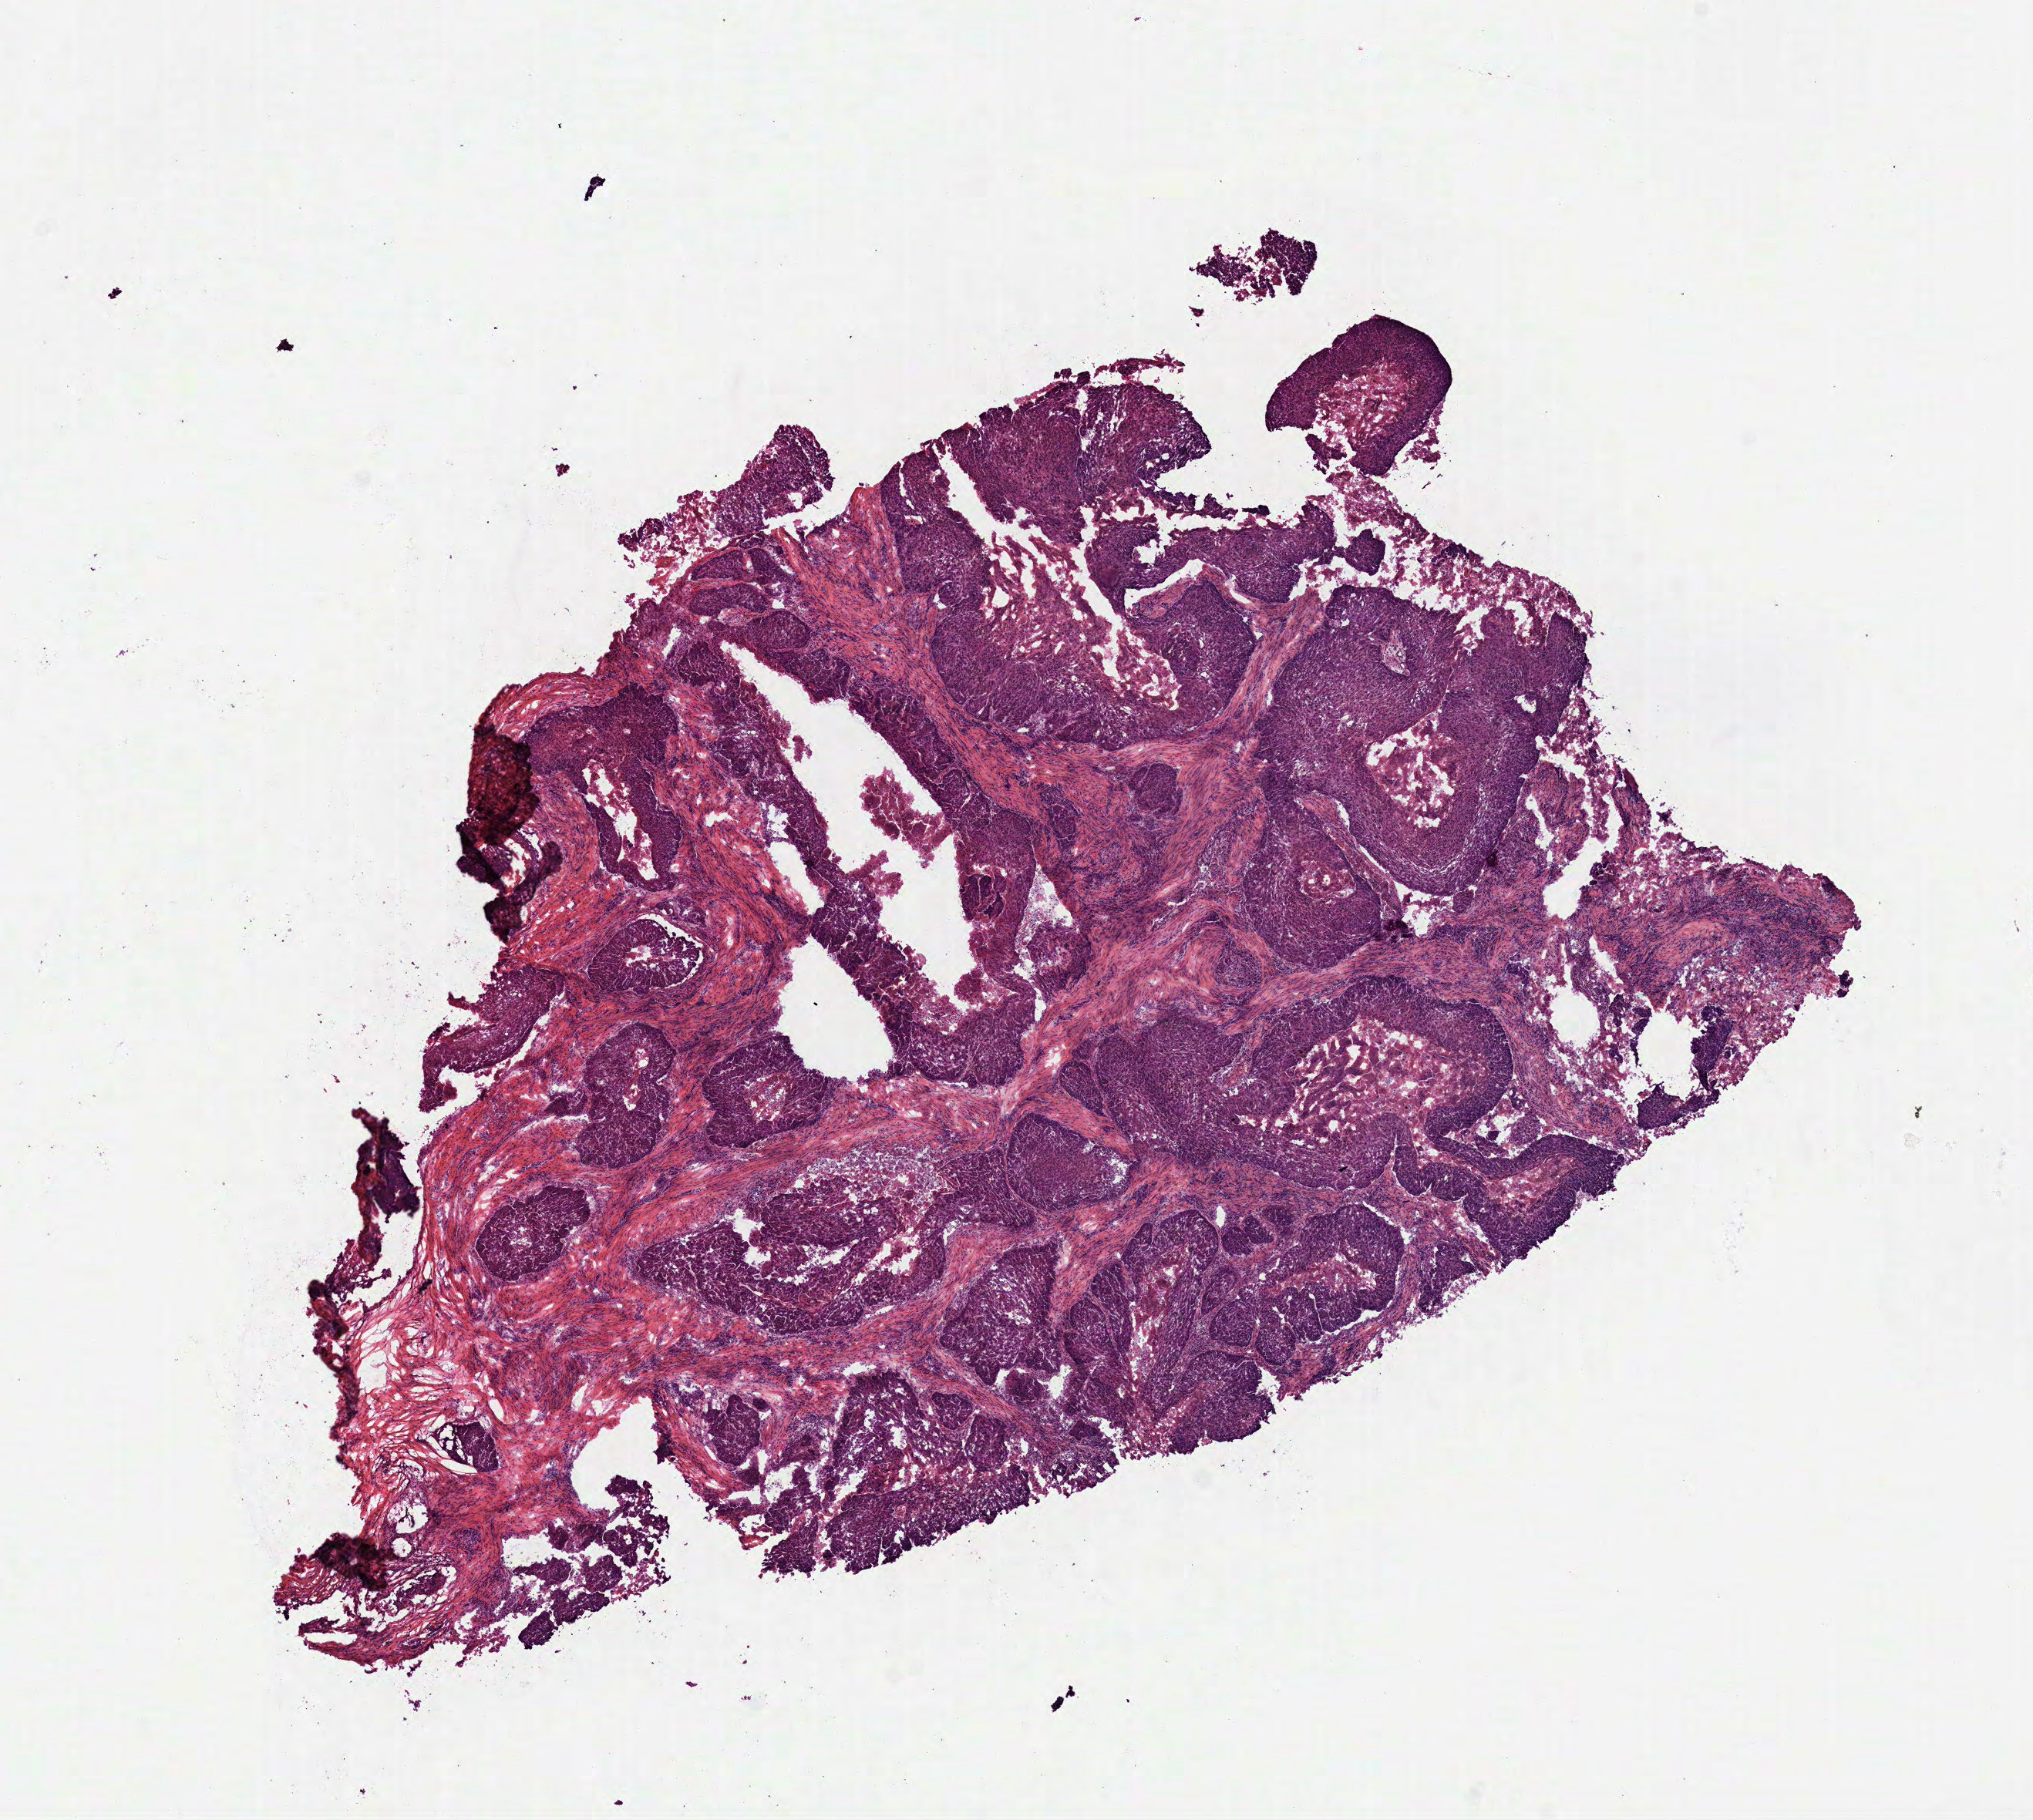
H&E whole-slide image — a low-resolution overview of the entire scanned area, about 10.6 x 9.5 mm (from a 40x scan), frozen section, primary tumour sample from the head and neck. Patient: male, age at initial diagnosis 68 years. Histologic grade: G2 (moderately differentiated). Slide review estimates, as recorded: tumour cells 85%, tumour nuclei 85%, normal cells 0%, stromal cells 0%, necrosis 15%. Infiltration values recorded for this section: lymphocyte infiltration 2%, monocyte infiltration 0%, neutrophil infiltration 22%.
Histologic diagnosis: Squamous cell carcinoma, NOS (floor of mouth, NOS). AJCC pathologic stage: IVA (7th edition). Lymph nodes positive (case pathology): 5 of 10 examined.